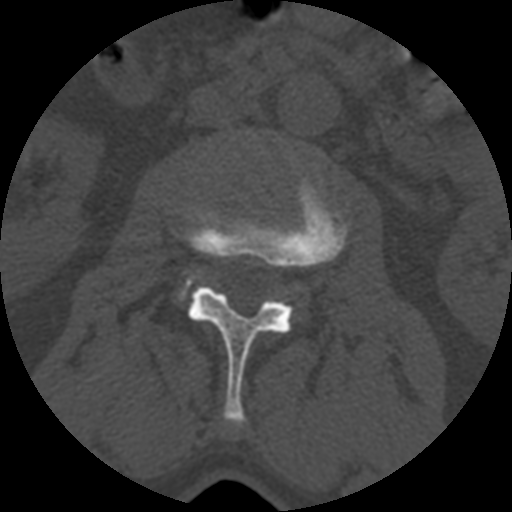
CT including the spine, one axial slice. Position 327 of 399 along the scan axis. Bone window (W 1800 / L 400 HU). 1.25 mm slice thickness. 512 × 512 image matrix. Patient age 71 years. From the clinical record (not read from this slice): primary cancer: prostate.
Outlined on this slice (semi-automatically segmented with operator editing):
- L2 vertebra: bounding box [x1, y1, x2, y2] px = [185, 179, 349, 427]
- L3 vertebra: [176, 271, 202, 301]